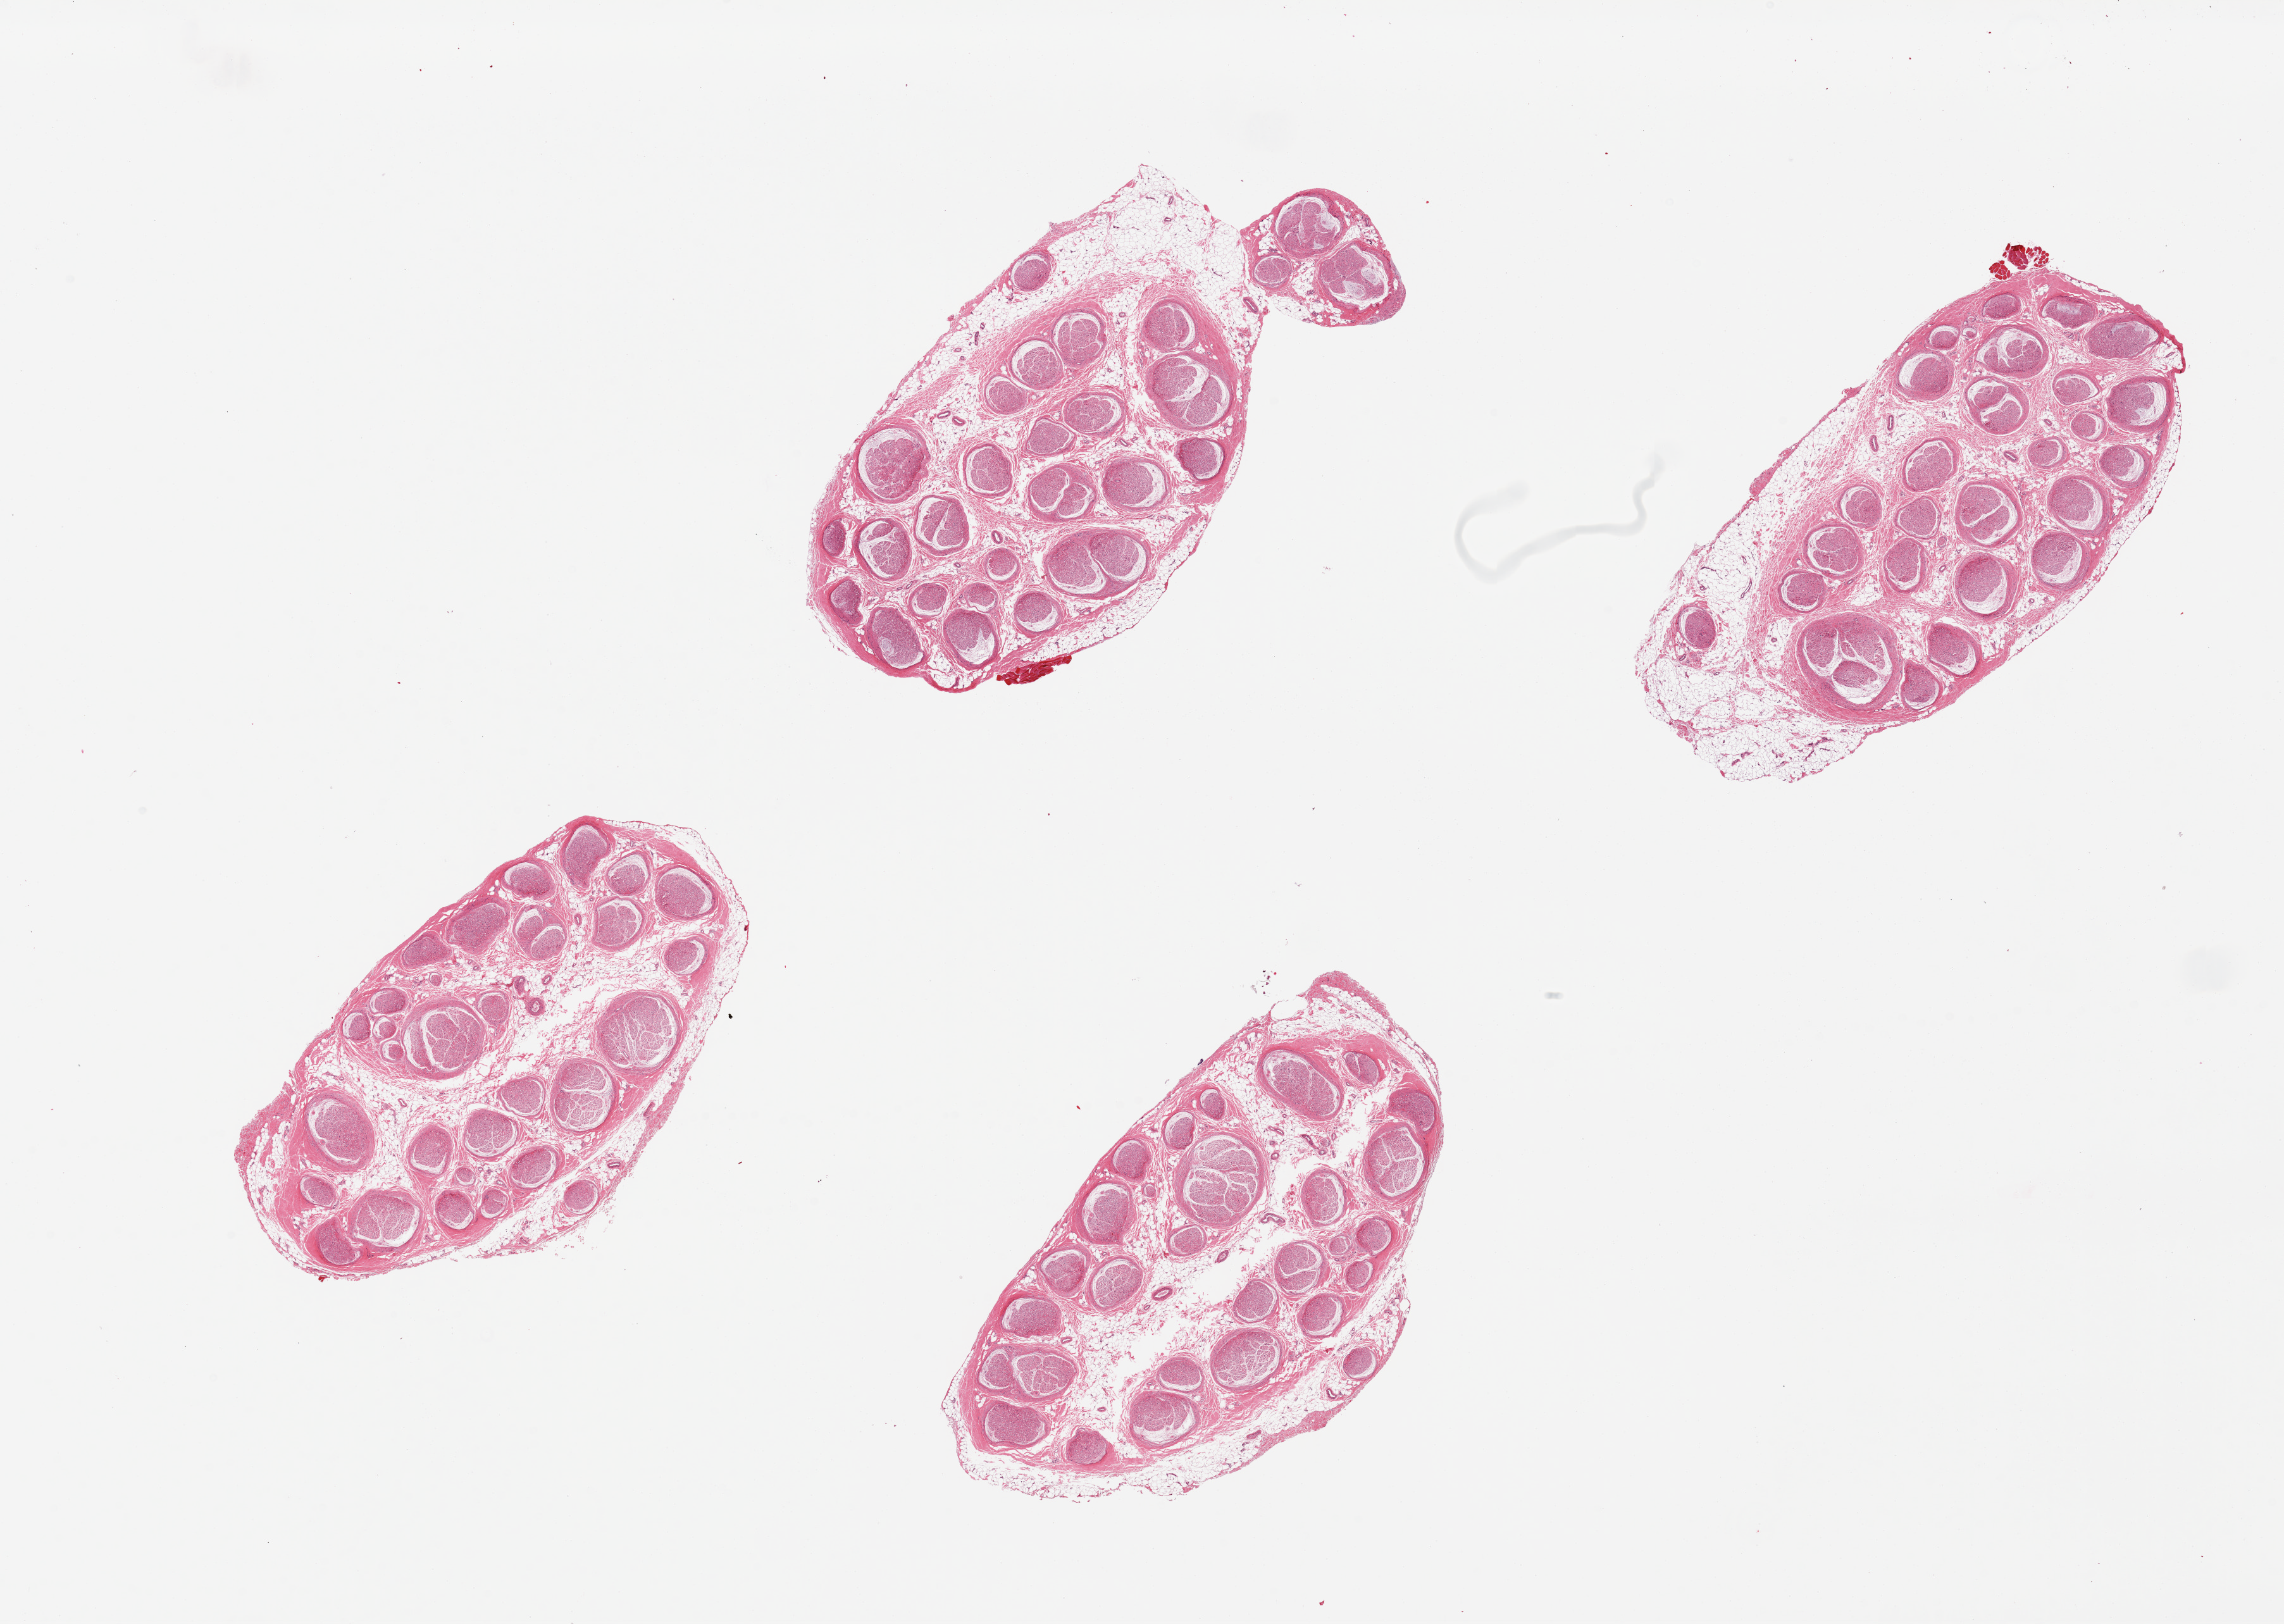
Whole-slide image, hematoxylin and eosin (H&E) stain, brightfield, whole scanned area (about 28.5 x 20.3 mm) shown as a low-resolution overview. PAXgene-fixed, paraffin-embedded tissue. Sampled site (target tissue): tibial nerve. Donor tissue sample. Donor sex: male.
Review note (as recorded): 4 pieces. up to 25% external fat.